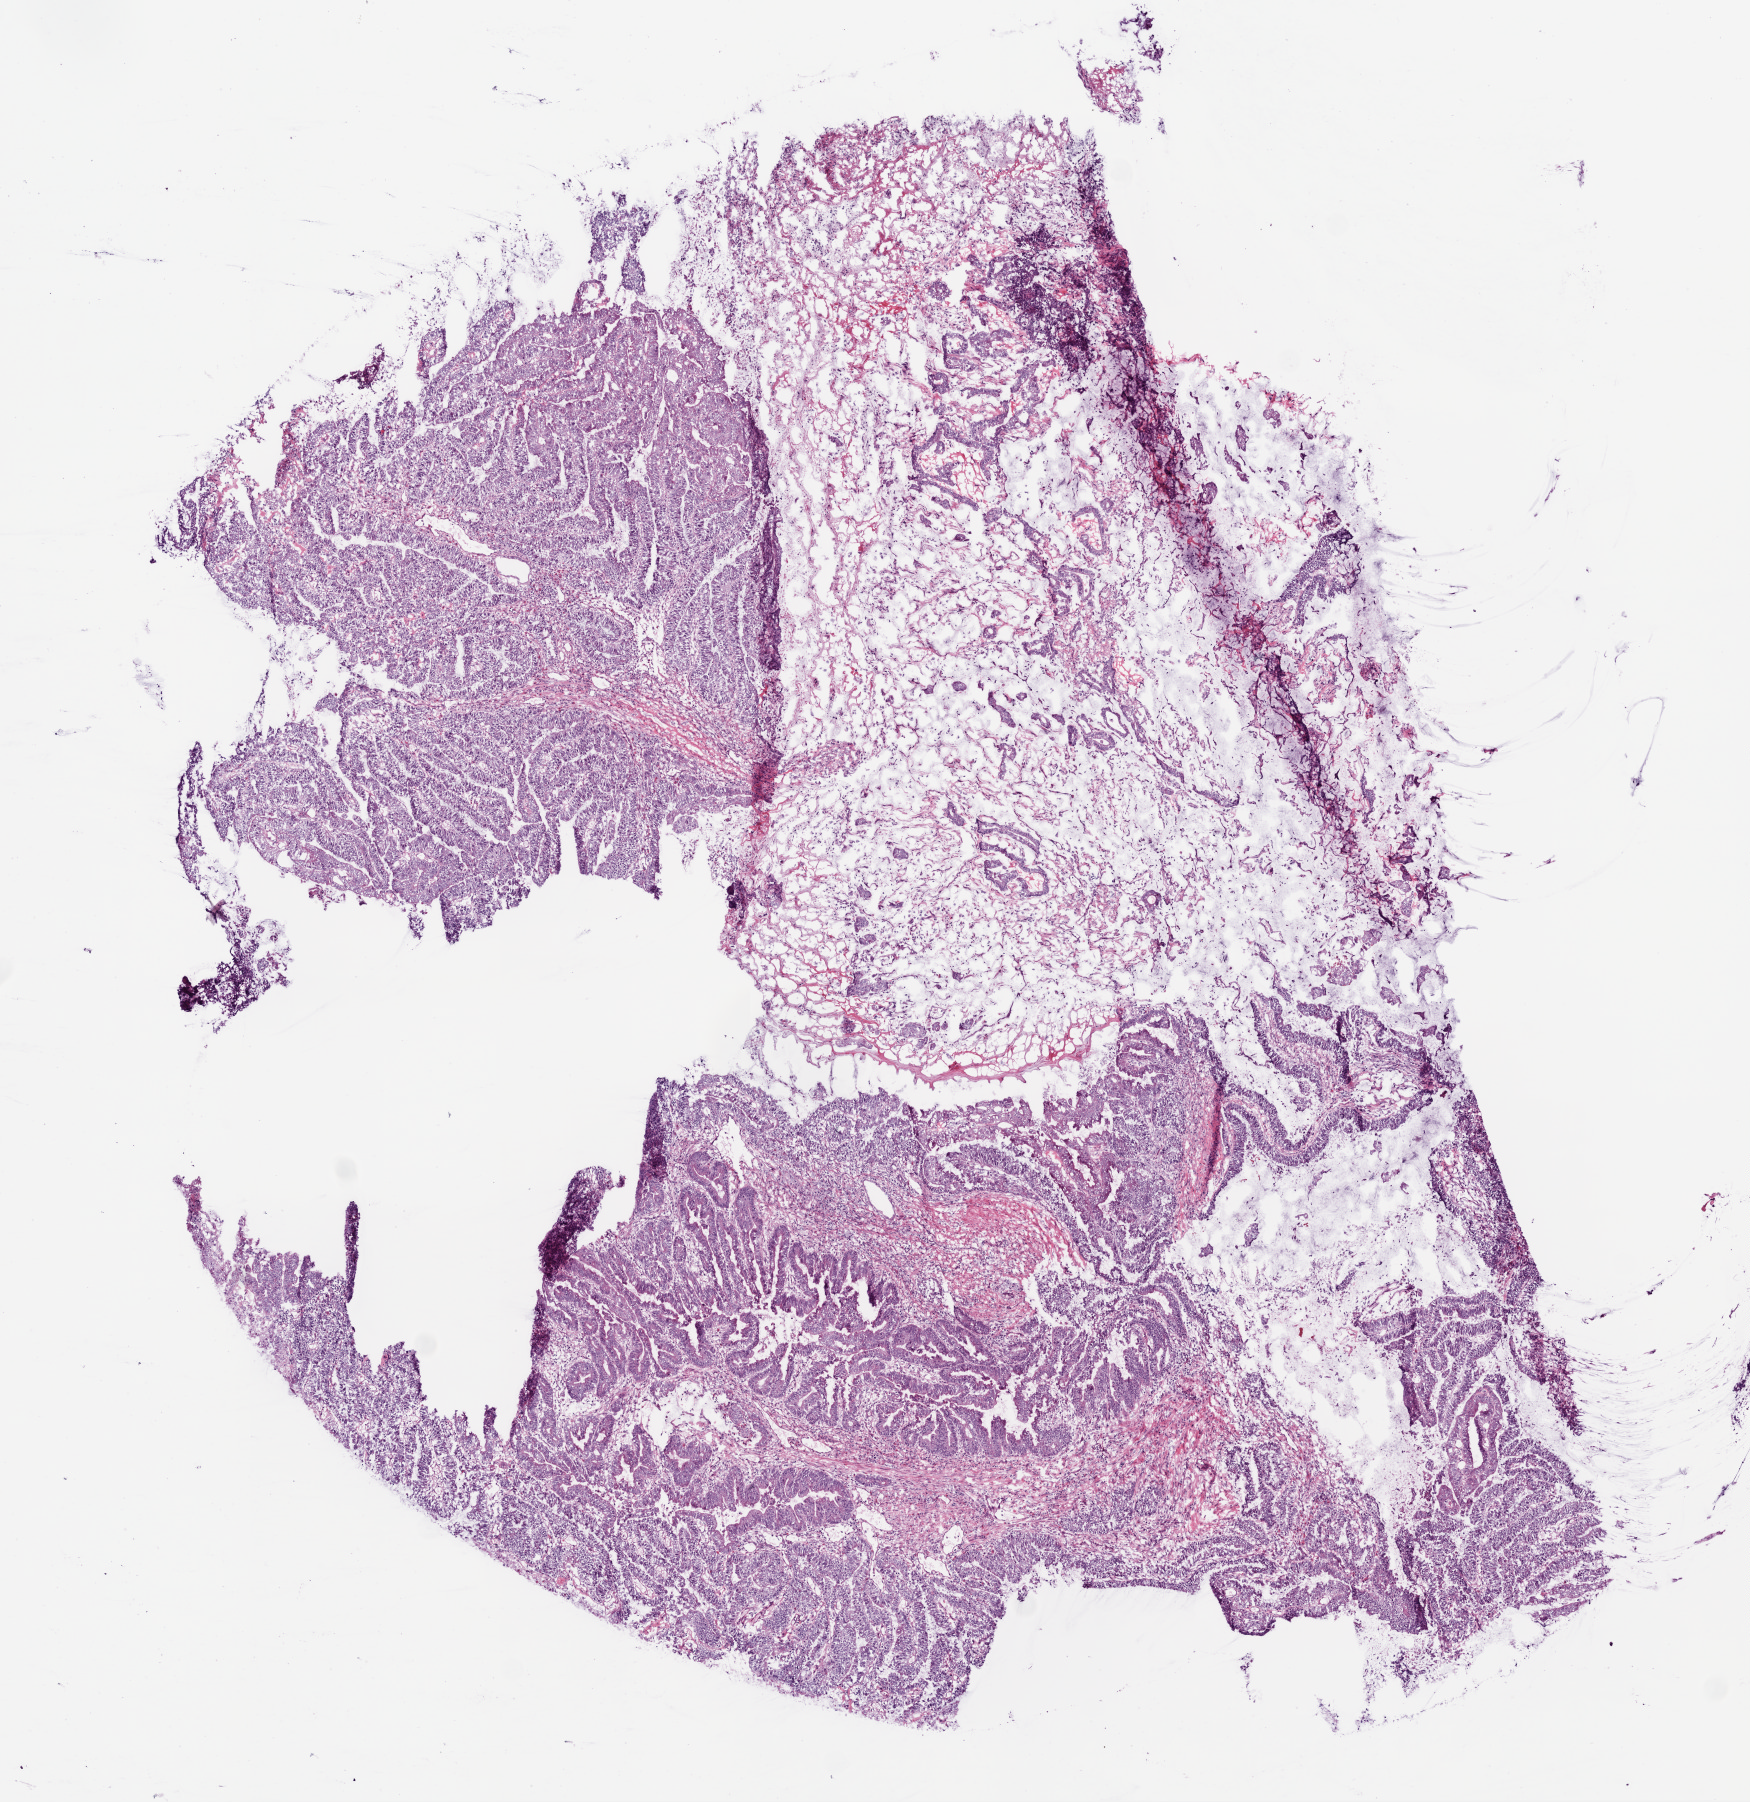
H&E-stained whole-slide image — low-resolution overview of the scanned area, about 7.0 x 7.2 mm; frozen section; colon, primary tumour sample. Male, age 69 years at initial diagnosis. Slide review estimates, as recorded: tumour cells 60%, tumour nuclei 70%.
Diagnosis: Mucinous adenocarcinoma.